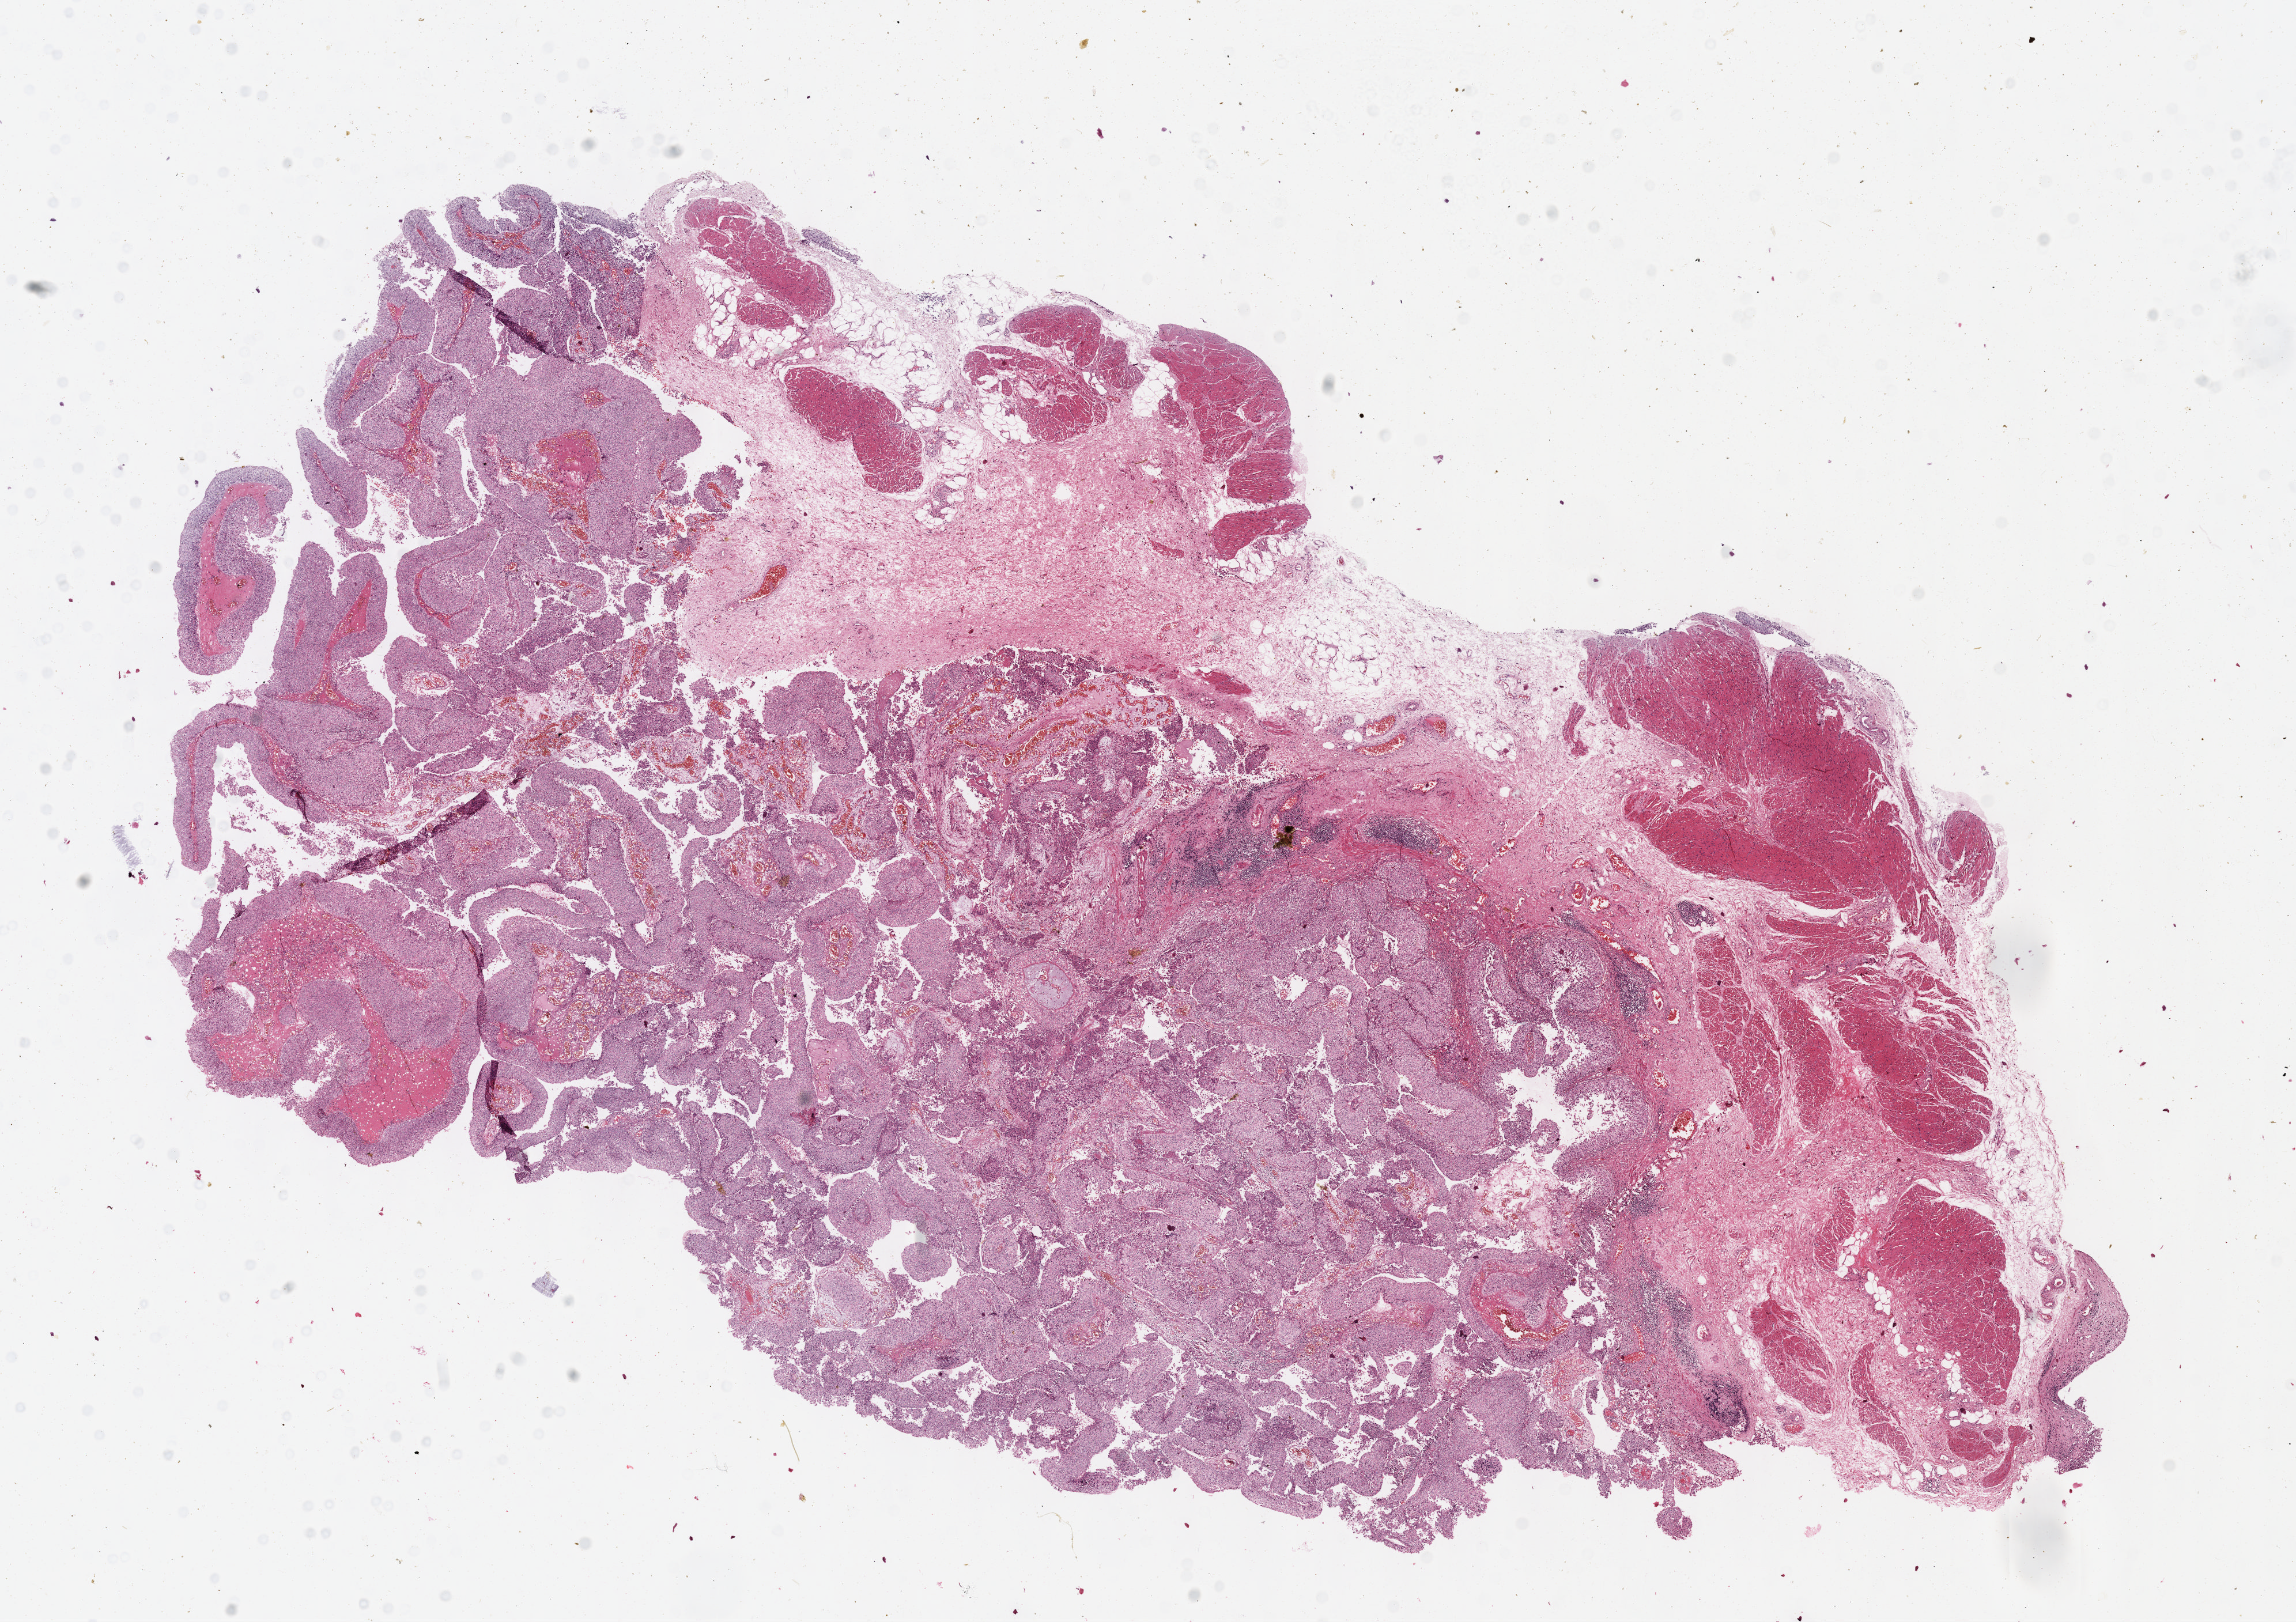
H&E-stained whole-slide image, whole scanned area (about 16.1 x 11.4 mm) shown as a low-resolution overview; FFPE section; bladder, primary tumour sample. Patient: male, age at initial diagnosis 52 years. Histologic grade: high grade.
Diagnosis: Papillary transitional cell carcinoma. AJCC pathologic stage: II (6th edition). TNM: T2 N0 M0.